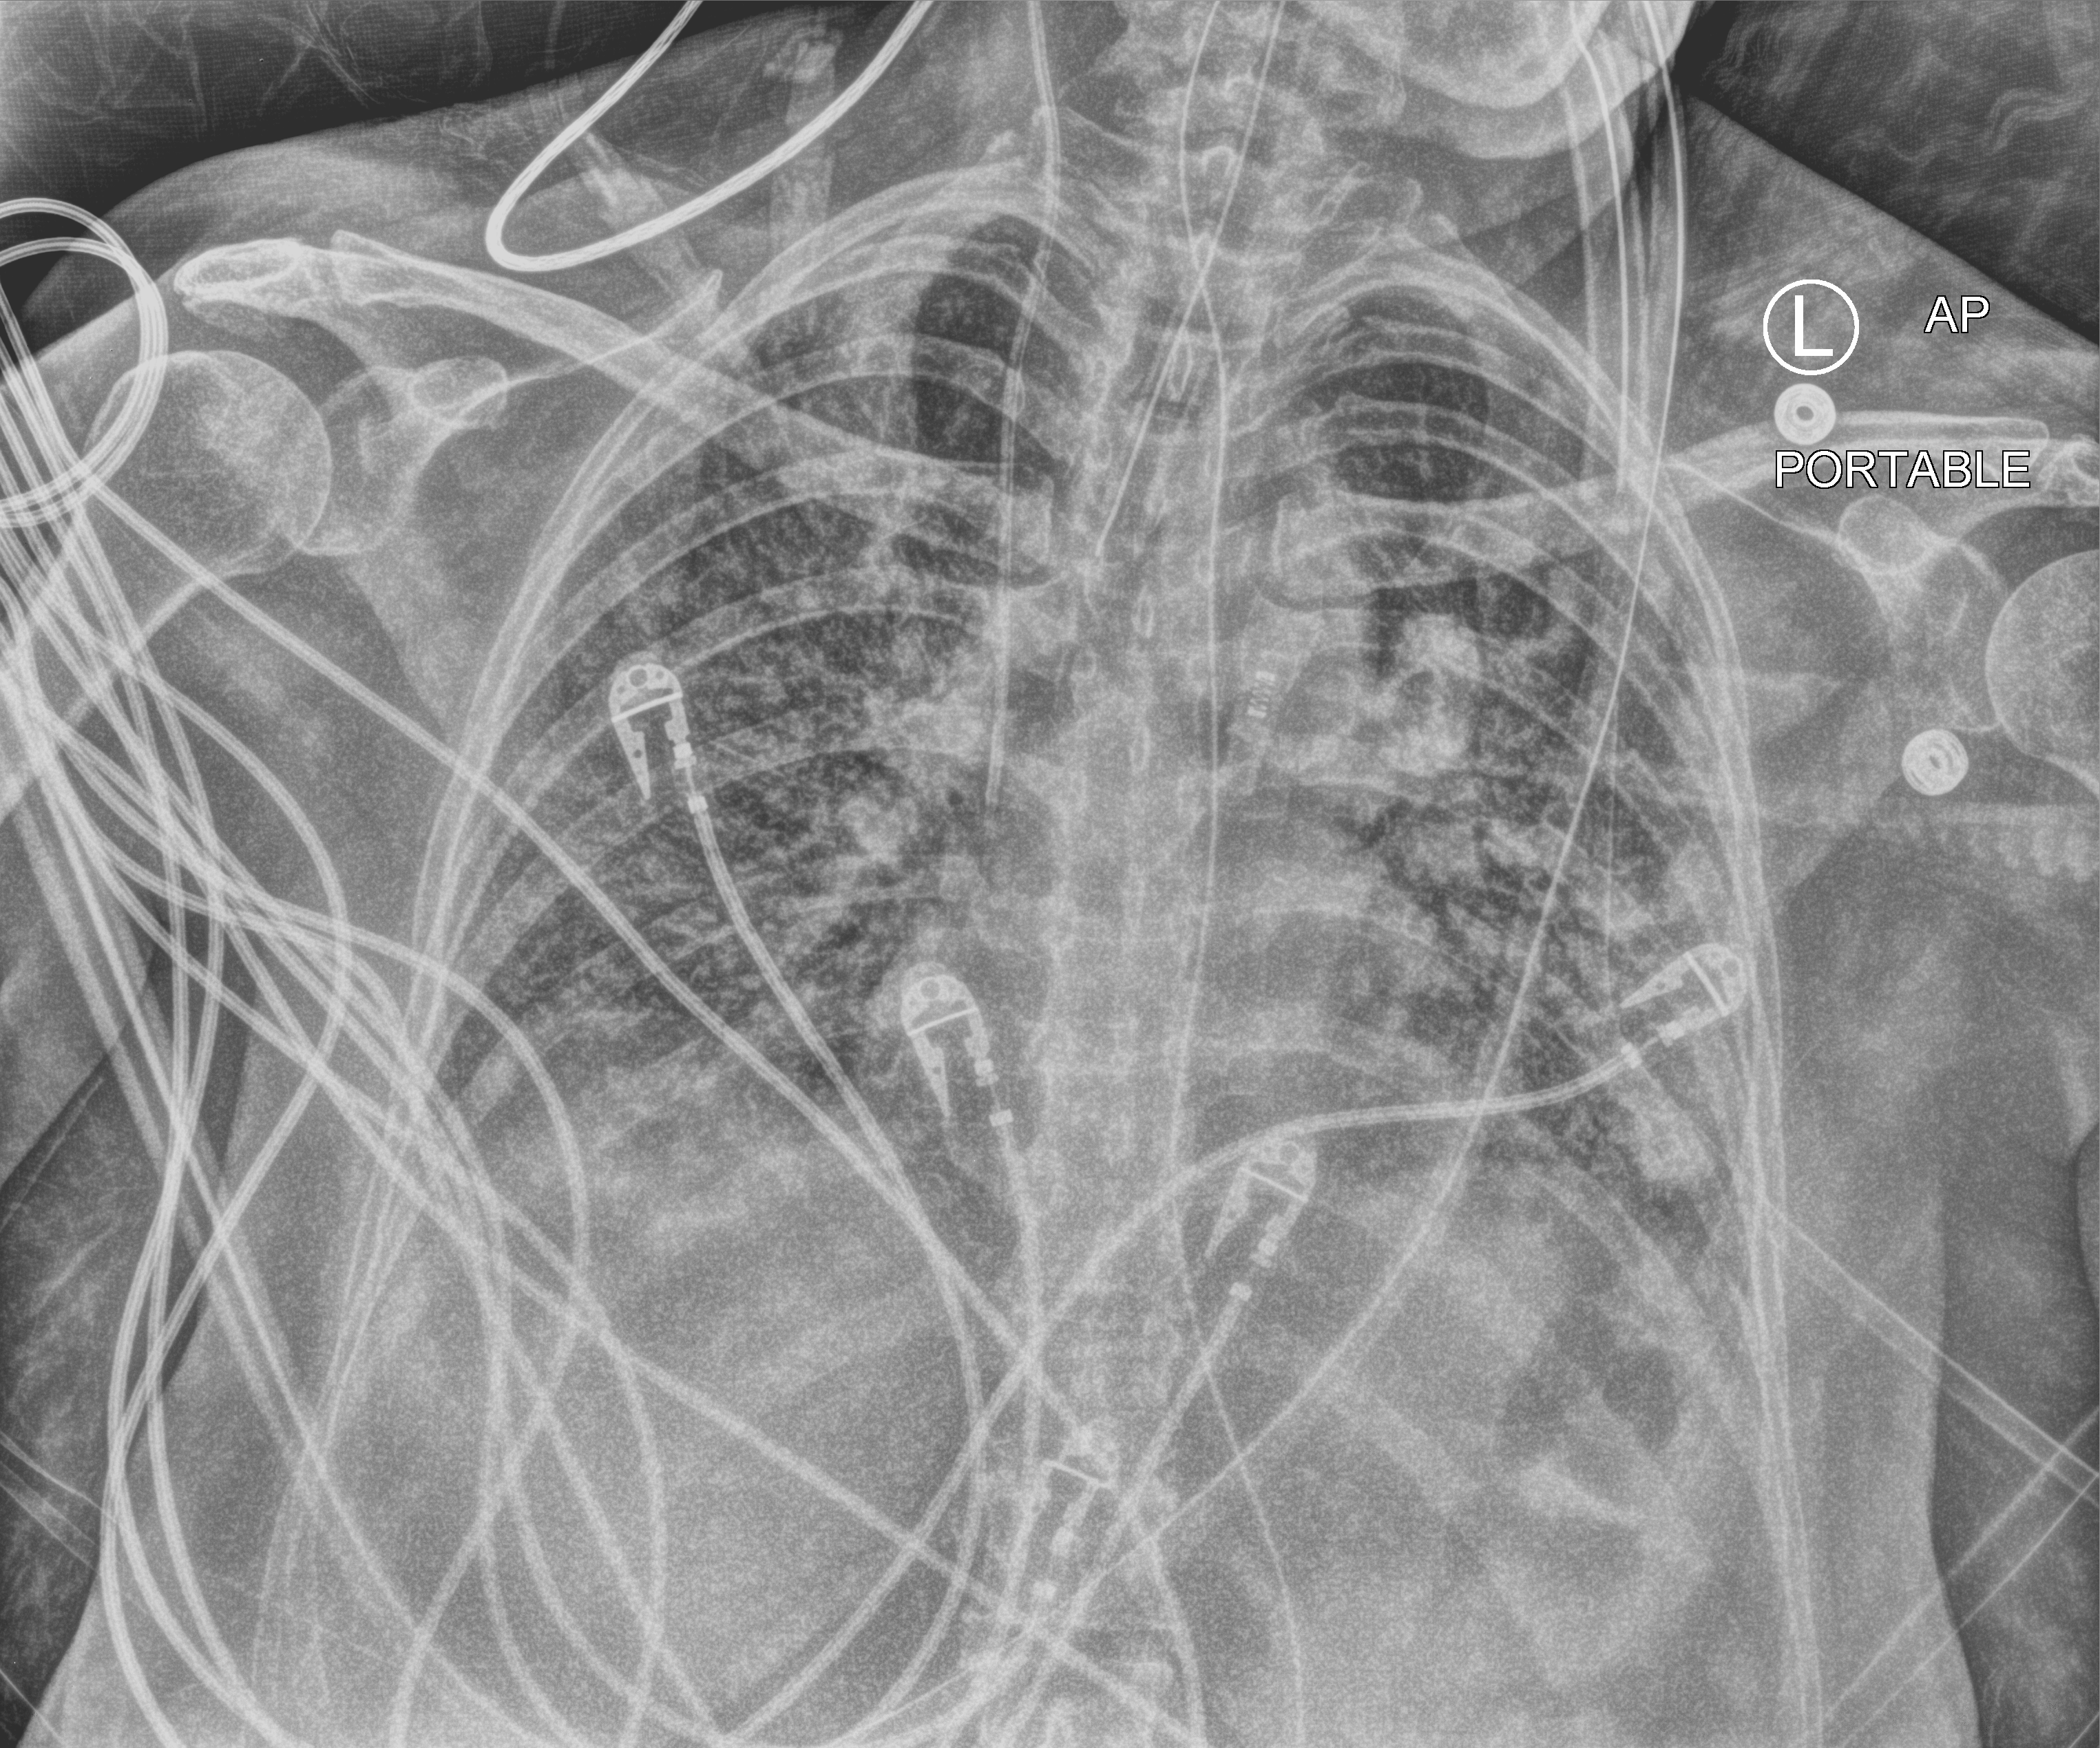
Chest X-ray (portable). Patient hospitalised with COVID-19; female, aged 60–74 years.
Admission-level facts for this patient (not findings on this image; timing relative to this image not recorded): mechanically ventilated during this hospital stay: yes; admitted to intensive care during this hospital stay: yes.